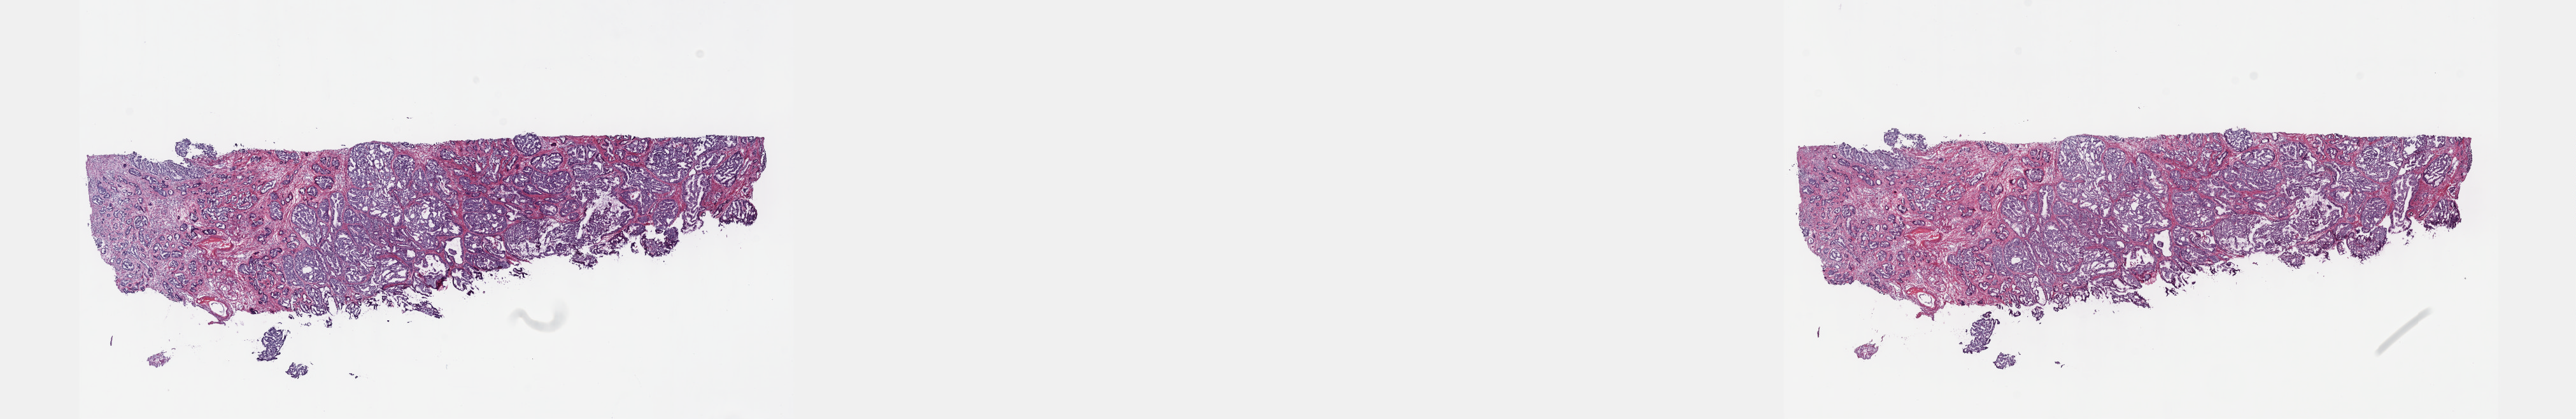
H&E-stained whole-slide image — low-resolution overview of the scanned area, about 32.7 x 5.3 mm (slide scanned at 40x); frozen section from the top of the tissue portion; primary tumour sample from the prostate. Patient: male, age at initial diagnosis 69 years. Gleason score: 8 (4+4). Composition of this section per pathologist review: tumour cells 70%, tumour nuclei 80%, normal cells 0%, stromal cells 30%, necrosis 0%. Infiltration values recorded for this section: lymphocyte infiltration 0%, monocyte infiltration 0%, neutrophil infiltration 0%.
- diagnosis: Adenocarcinoma, NOS (prostate gland)
- laterality: bilateral
- lymph nodes positive (case pathology): 0 of 9 examined